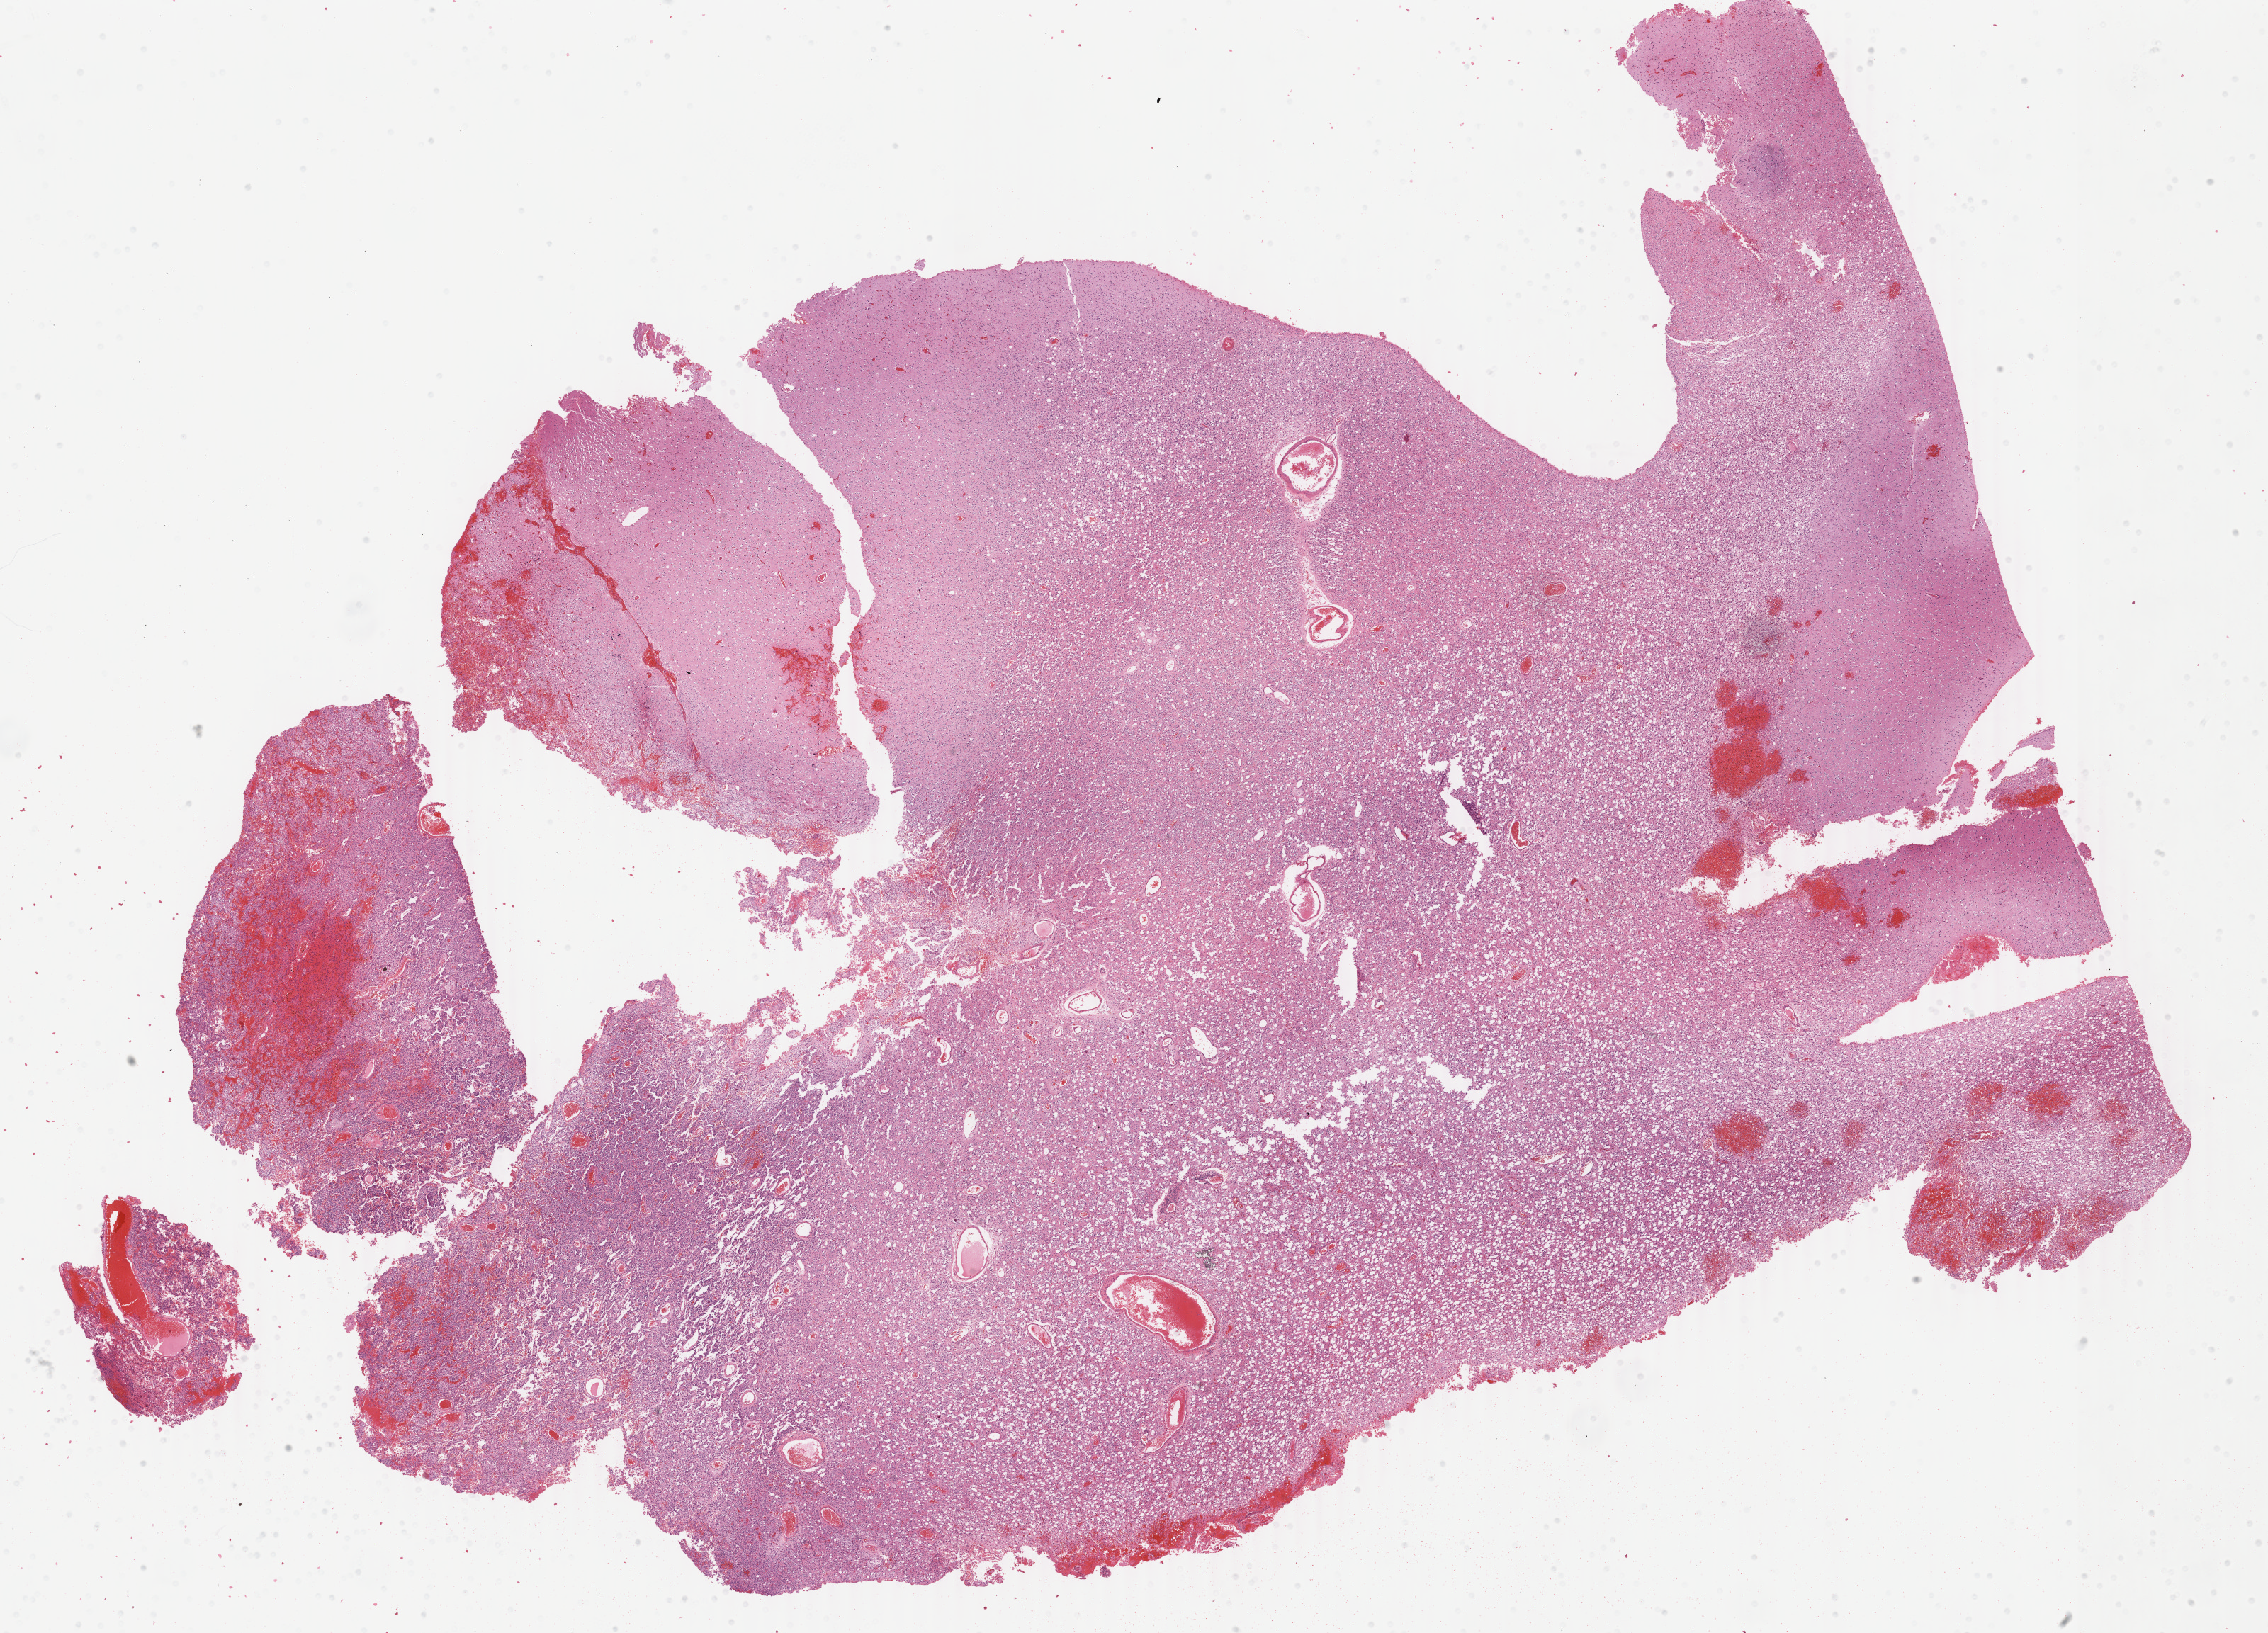
Hematoxylin and eosin (H&E) stained whole-slide image, a low-resolution overview of the entire scanned area, about 25.5 x 18.3 mm (acquisition: 40x scan); formalin-fixed paraffin-embedded (FFPE) diagnostic section; sample: primary tumour, brain. Patient: male, age at initial diagnosis 32 years. Histologic grade: G3 (poorly differentiated).
Histologic diagnosis: Oligodendroglioma, anaplastic (cerebrum).